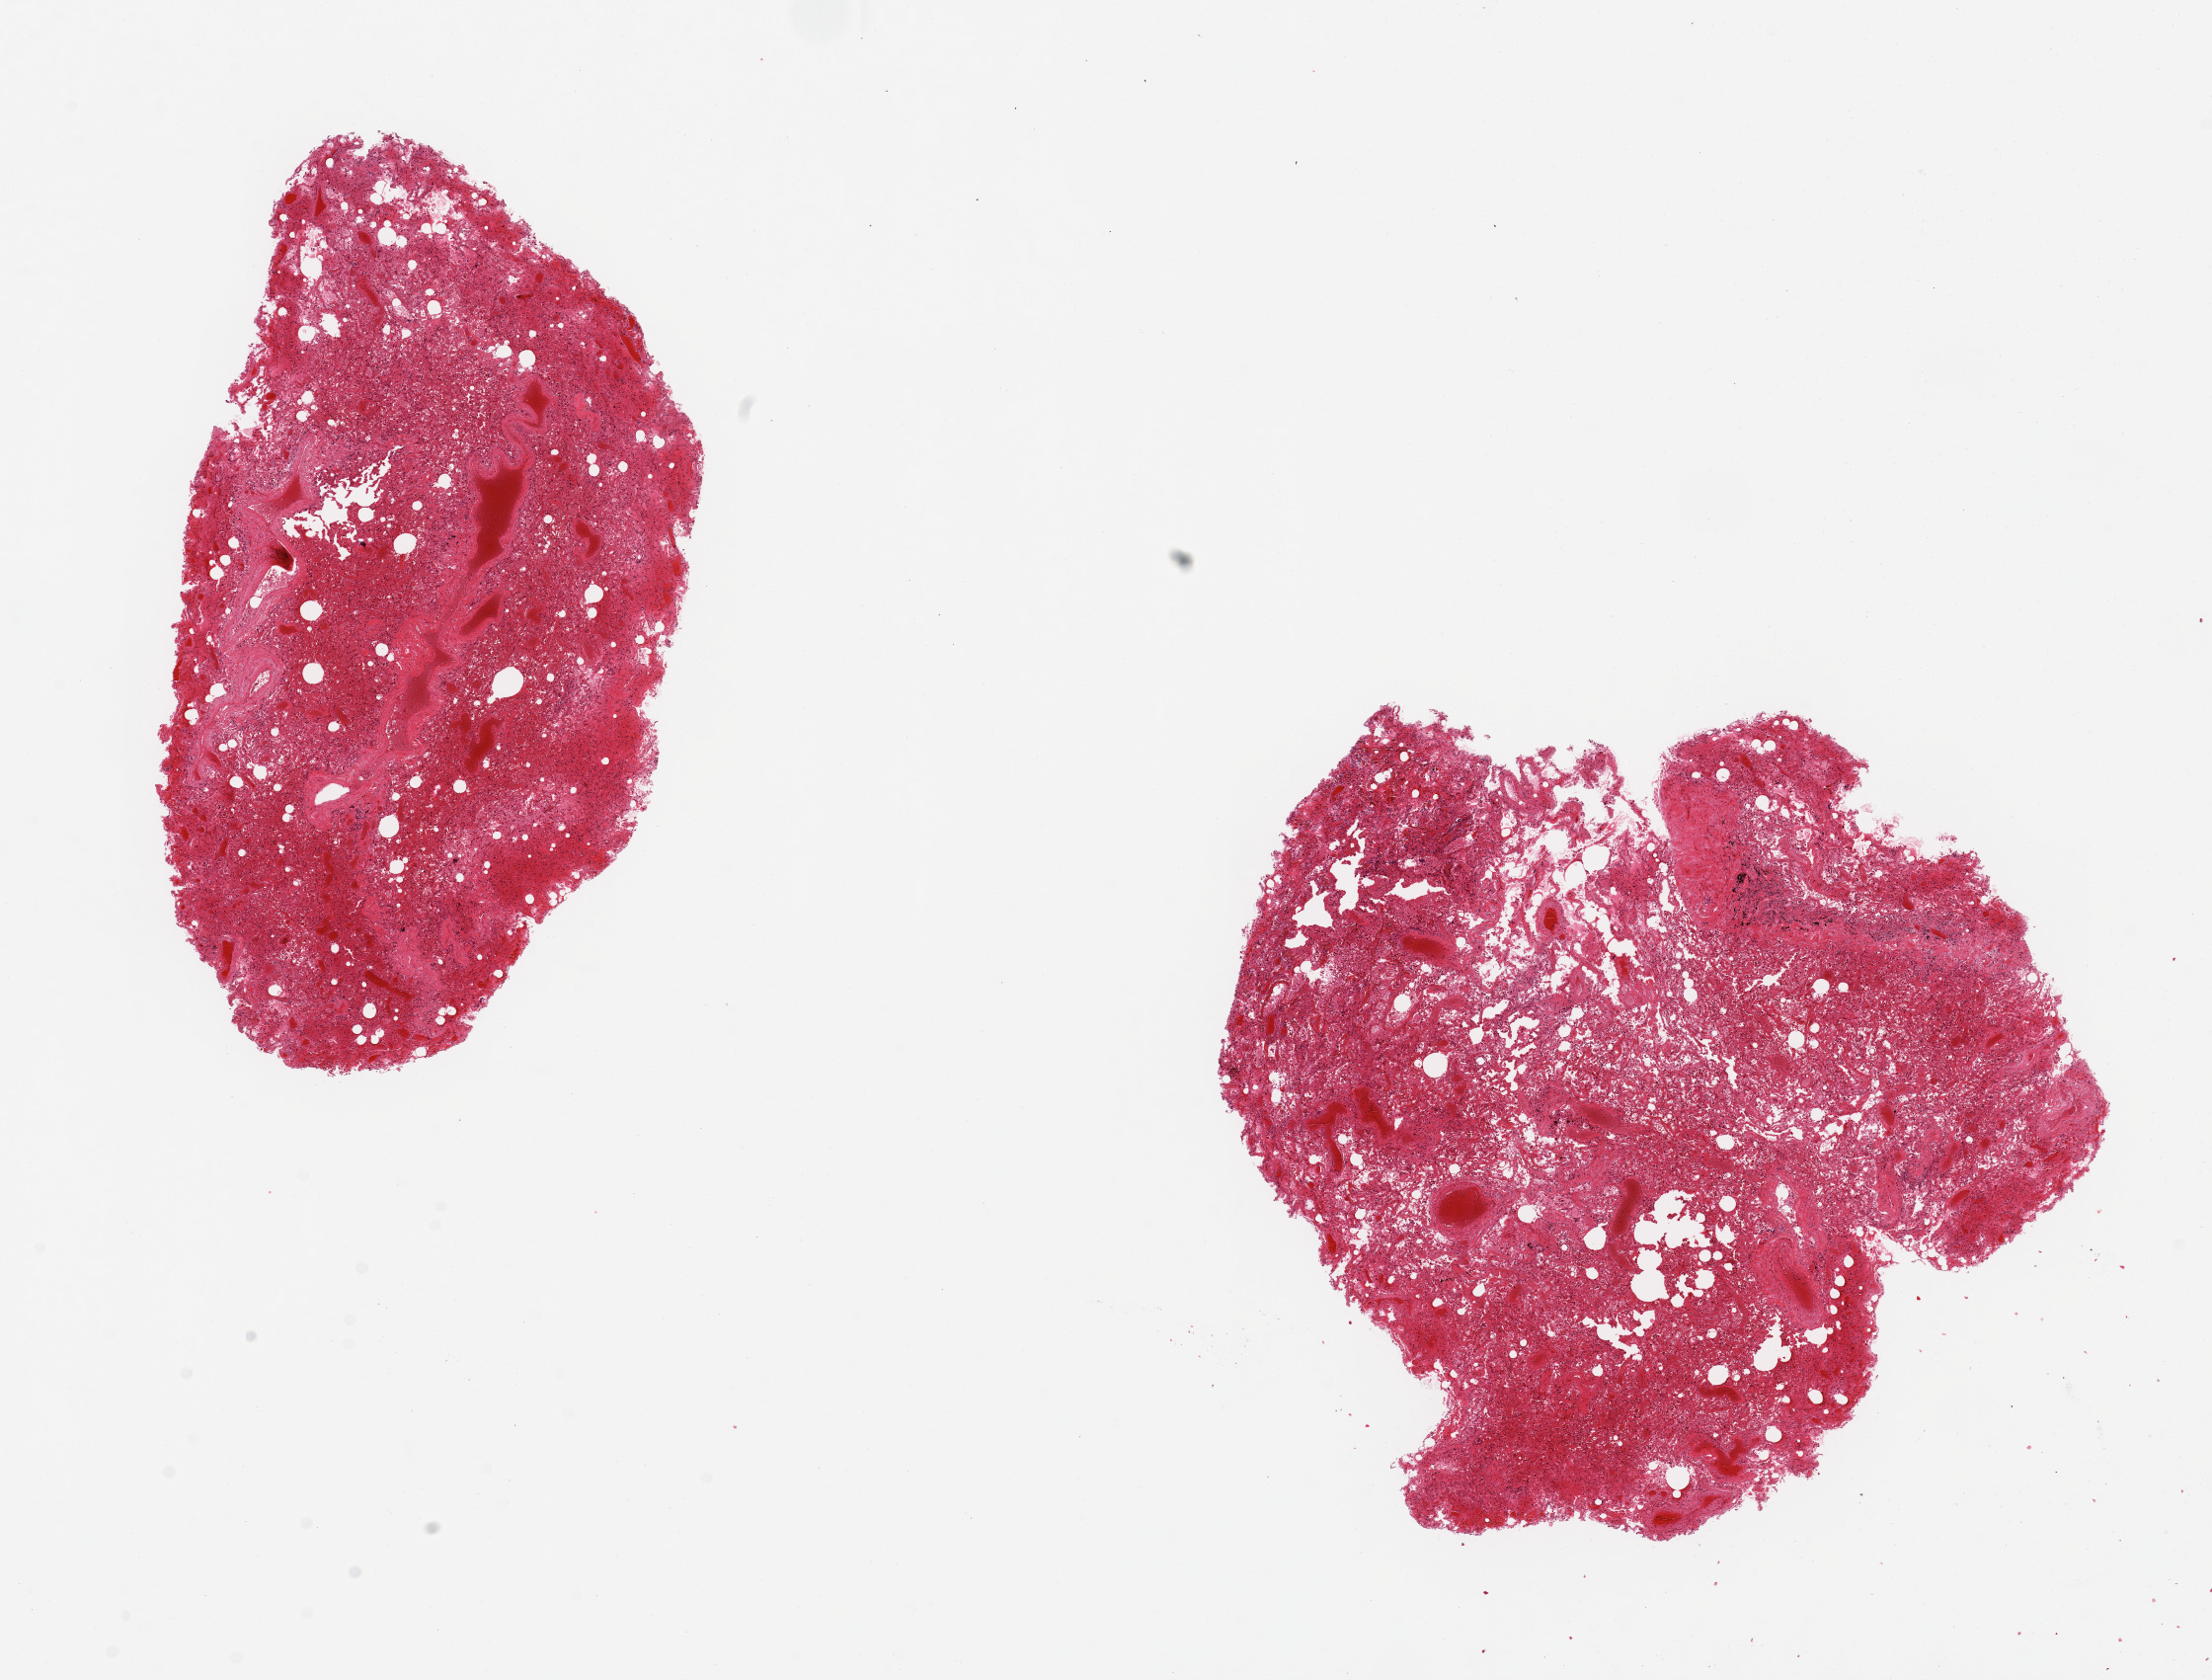
Digitized haematoxylin and eosin-stained section — shown as a low-resolution overview of the whole scanned area (about 17.7 x 13.5 mm, slide scanned at 20x), PAXgene-fixed paraffin-embedded (PFPE) section, target tissue: lung, tissue donor sample. Donor sex: male.
Pathologist's review note for this sample: 2 aliquots, ~7x6mm. Badly autolyzed, severe congestion.